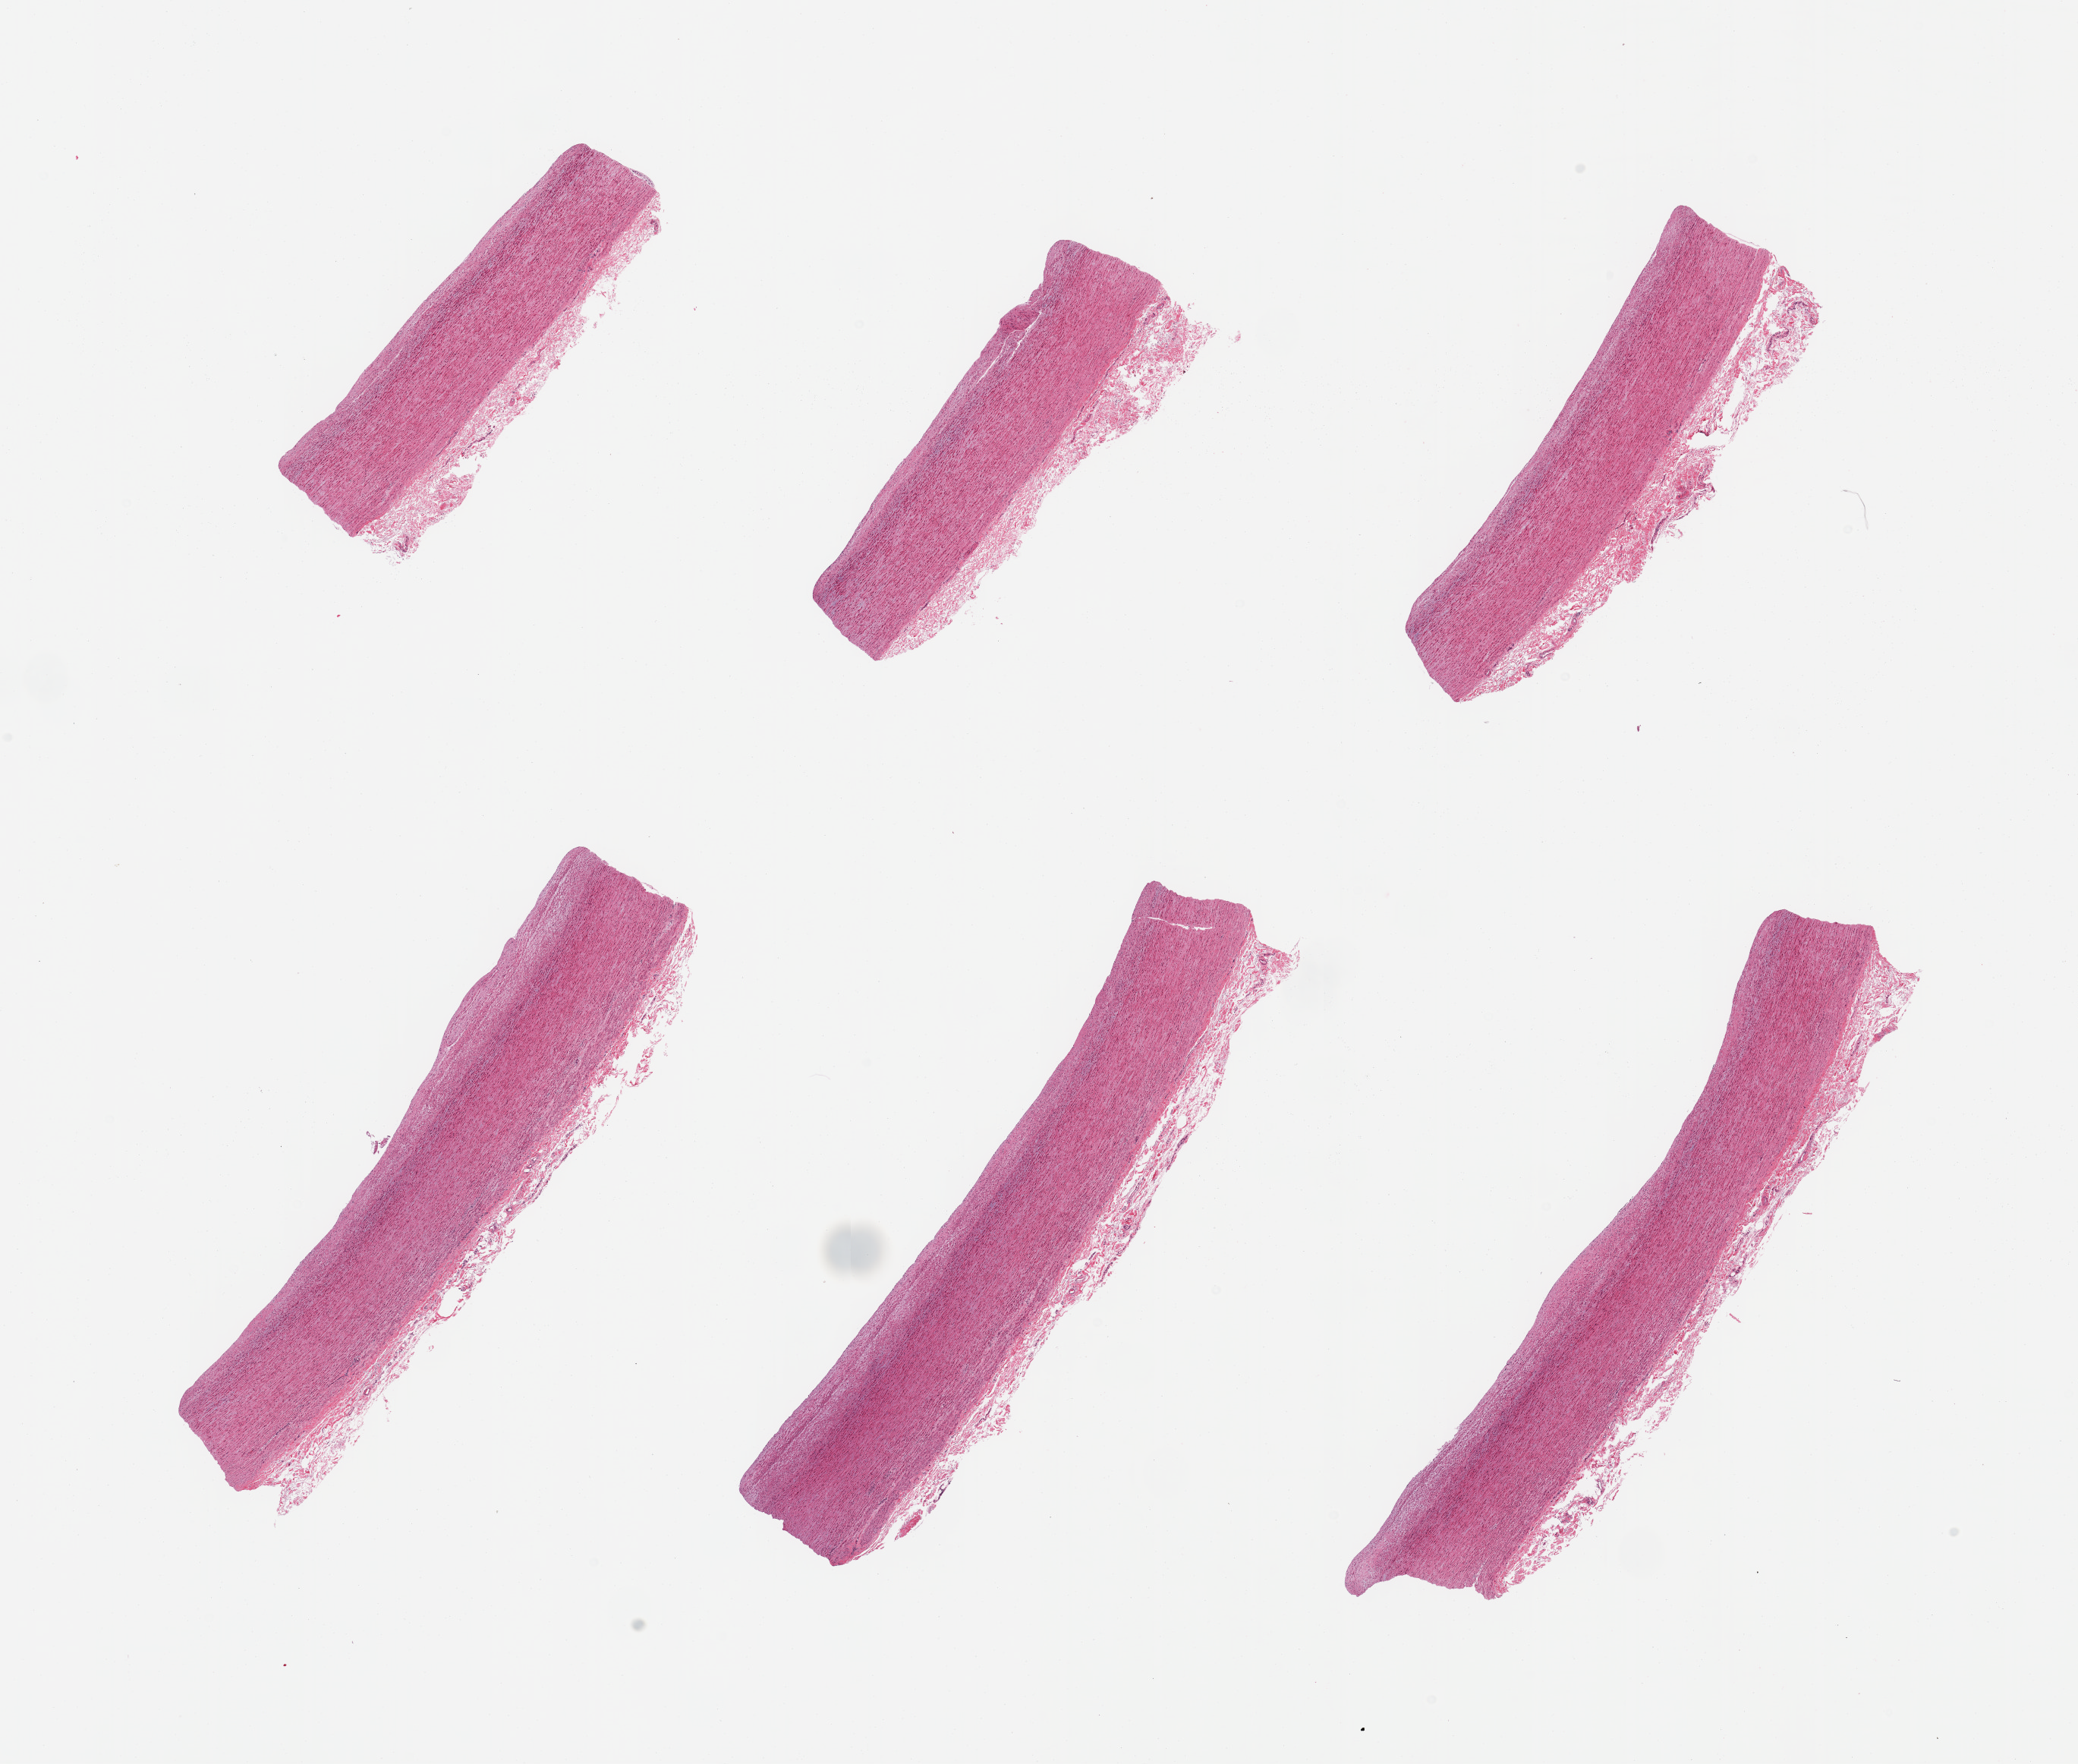
Digitized hematoxylin and eosin (H&E)-stained section, low-resolution overview of the scanned area, about 21.7 x 18.4 mm (slide scanned at 20x); PAXgene-fixed, paraffin-embedded tissue; sampled site (target tissue): aorta; tissue donor sample. Donor: male.
Reviewer comment on this tissue sample: 6 pieces. atherosis up to ~0.2mm.